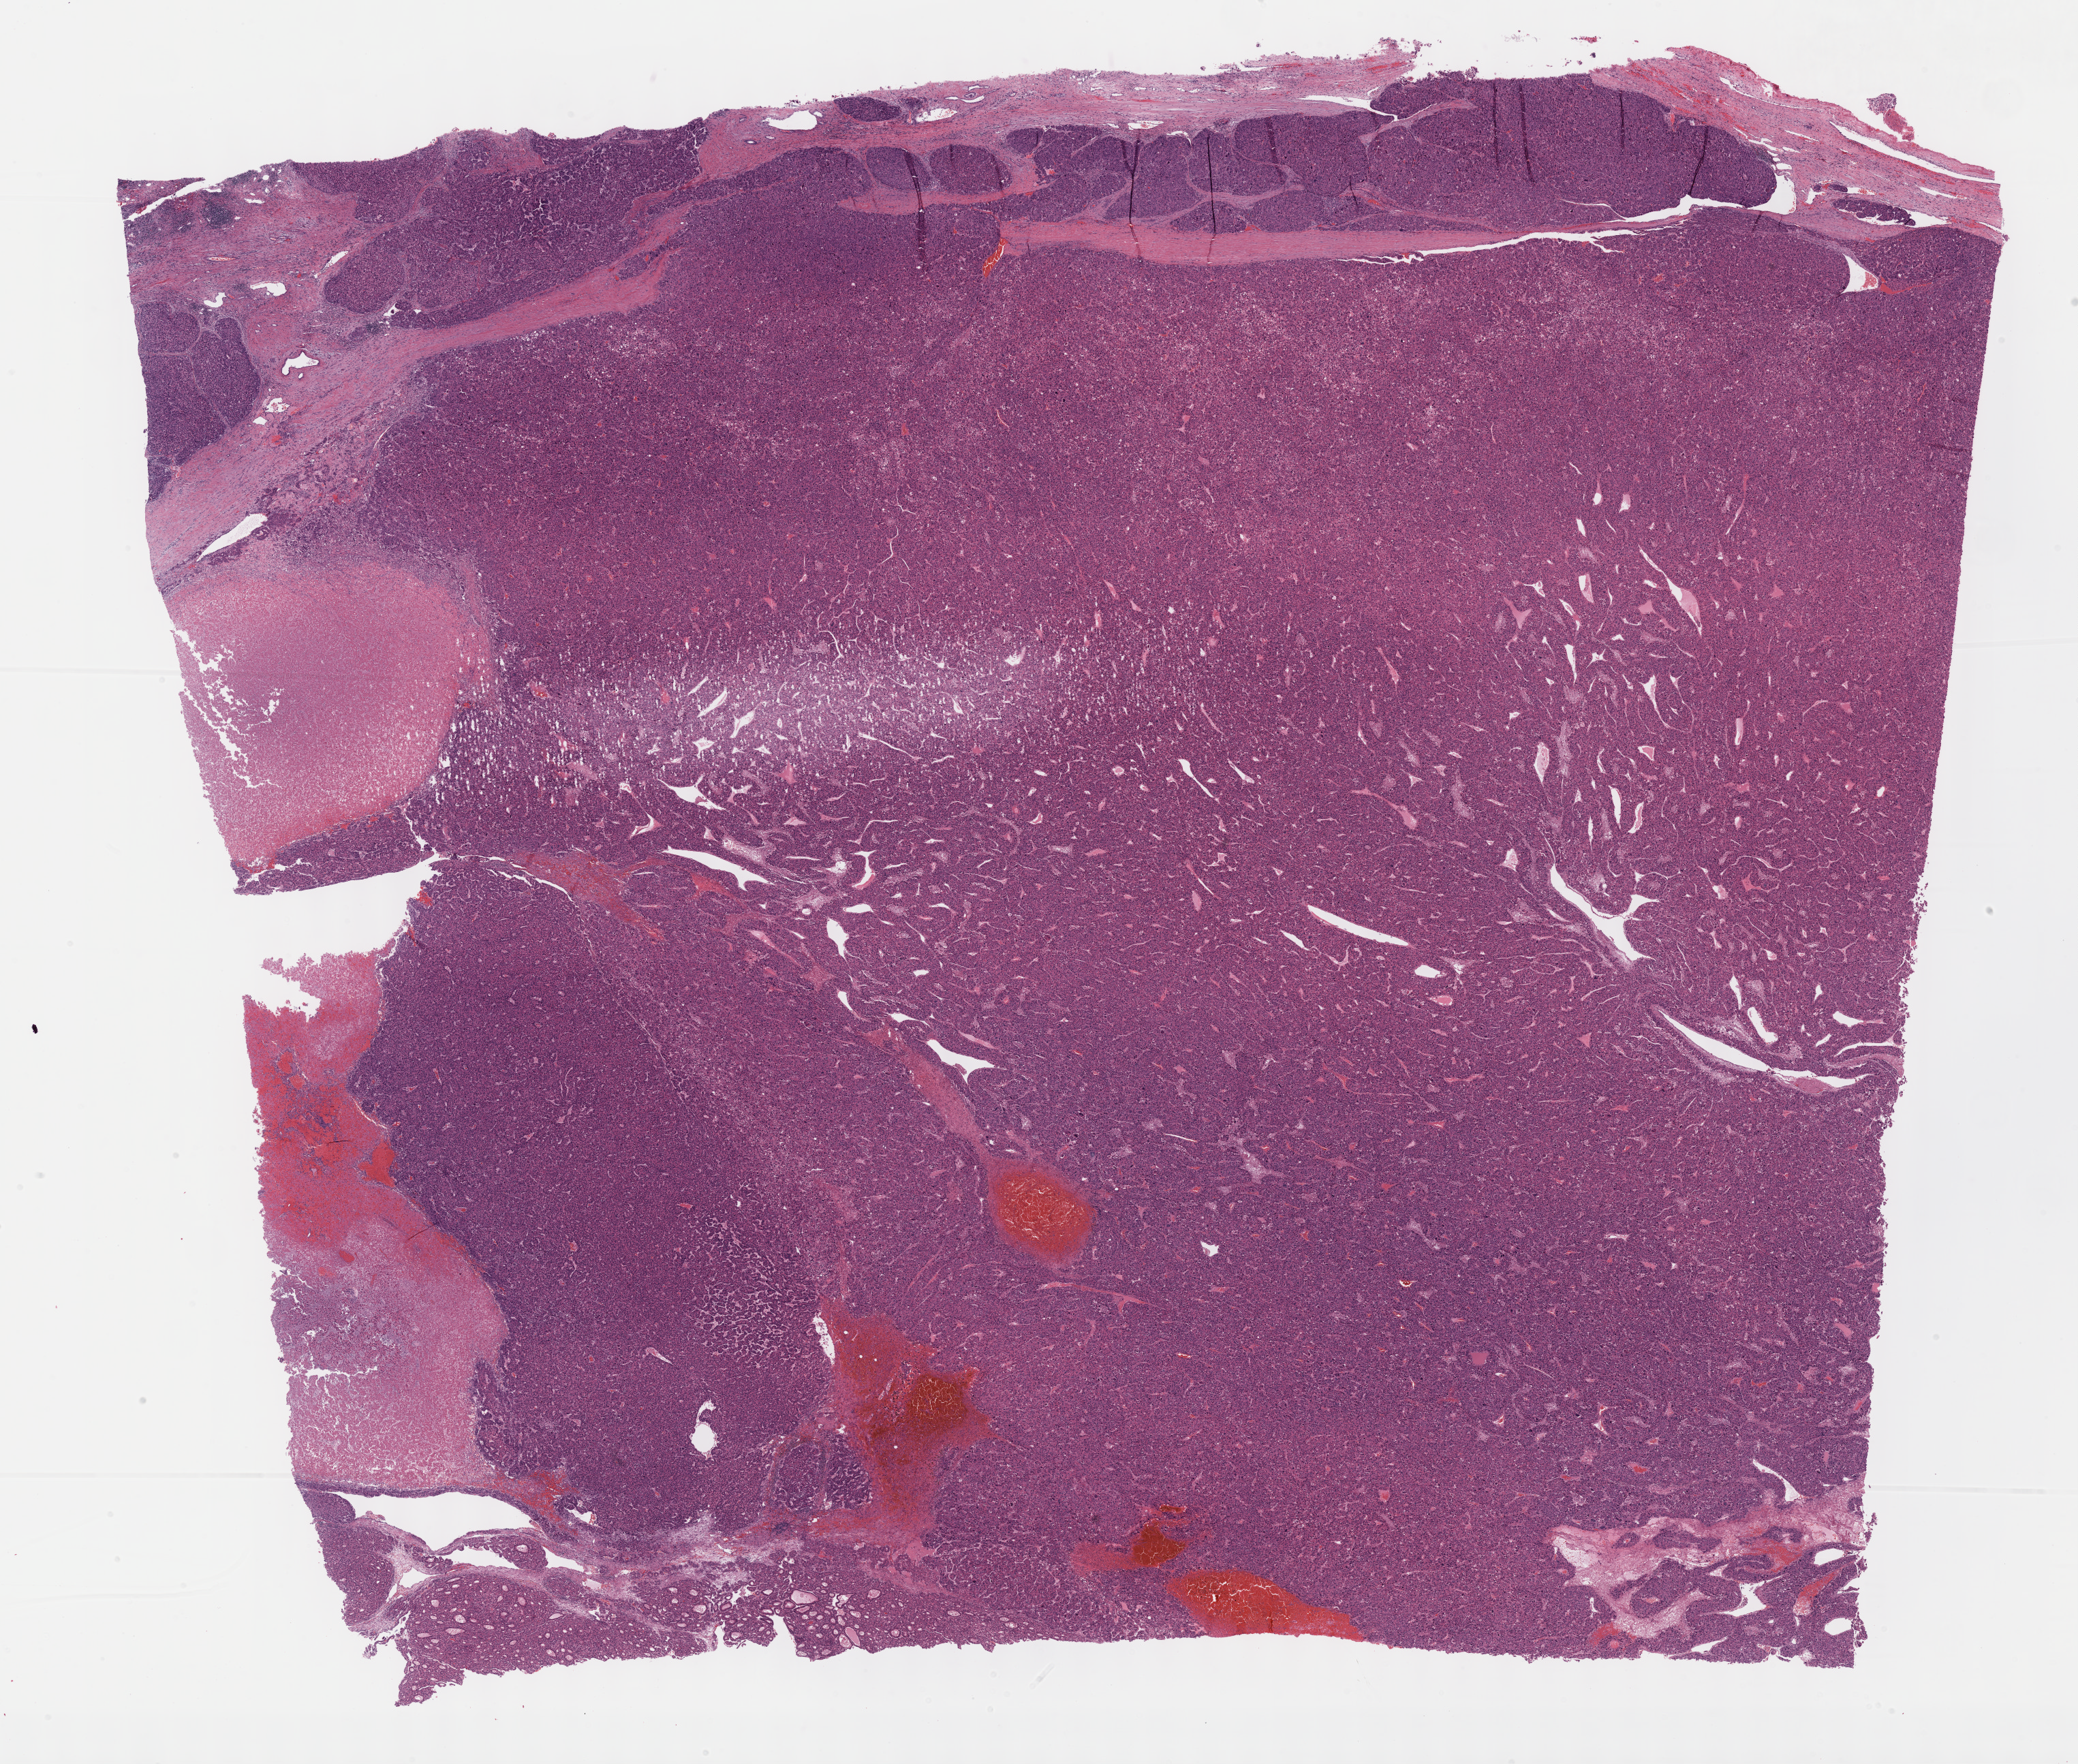
Whole-slide histology image, H&E — low-resolution overview of the scanned area, about 24.7 x 20.9 mm (acquisition: 40x scan); formalin-fixed paraffin-embedded (FFPE) diagnostic section; primary tumour sample from the liver. Male, age 67 years at initial diagnosis.
Diagnosis: Hepatocellular carcinoma, NOS.